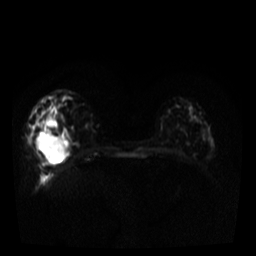
Breast MRI, one axial slice; slice 12 of 34 in the series (ordered by position); diffusion-weighted series; image 2 of 4 stored at this slice position (different b-values; order by instance number); 3 T; 256 × 256 image matrix. Female patient.
Annotated regions visible in this slice (manually delineated by an expert):
- tumour on diffusion-weighted imaging: bounding box <35,133,66,160> (left, top, right, bottom; pixels)